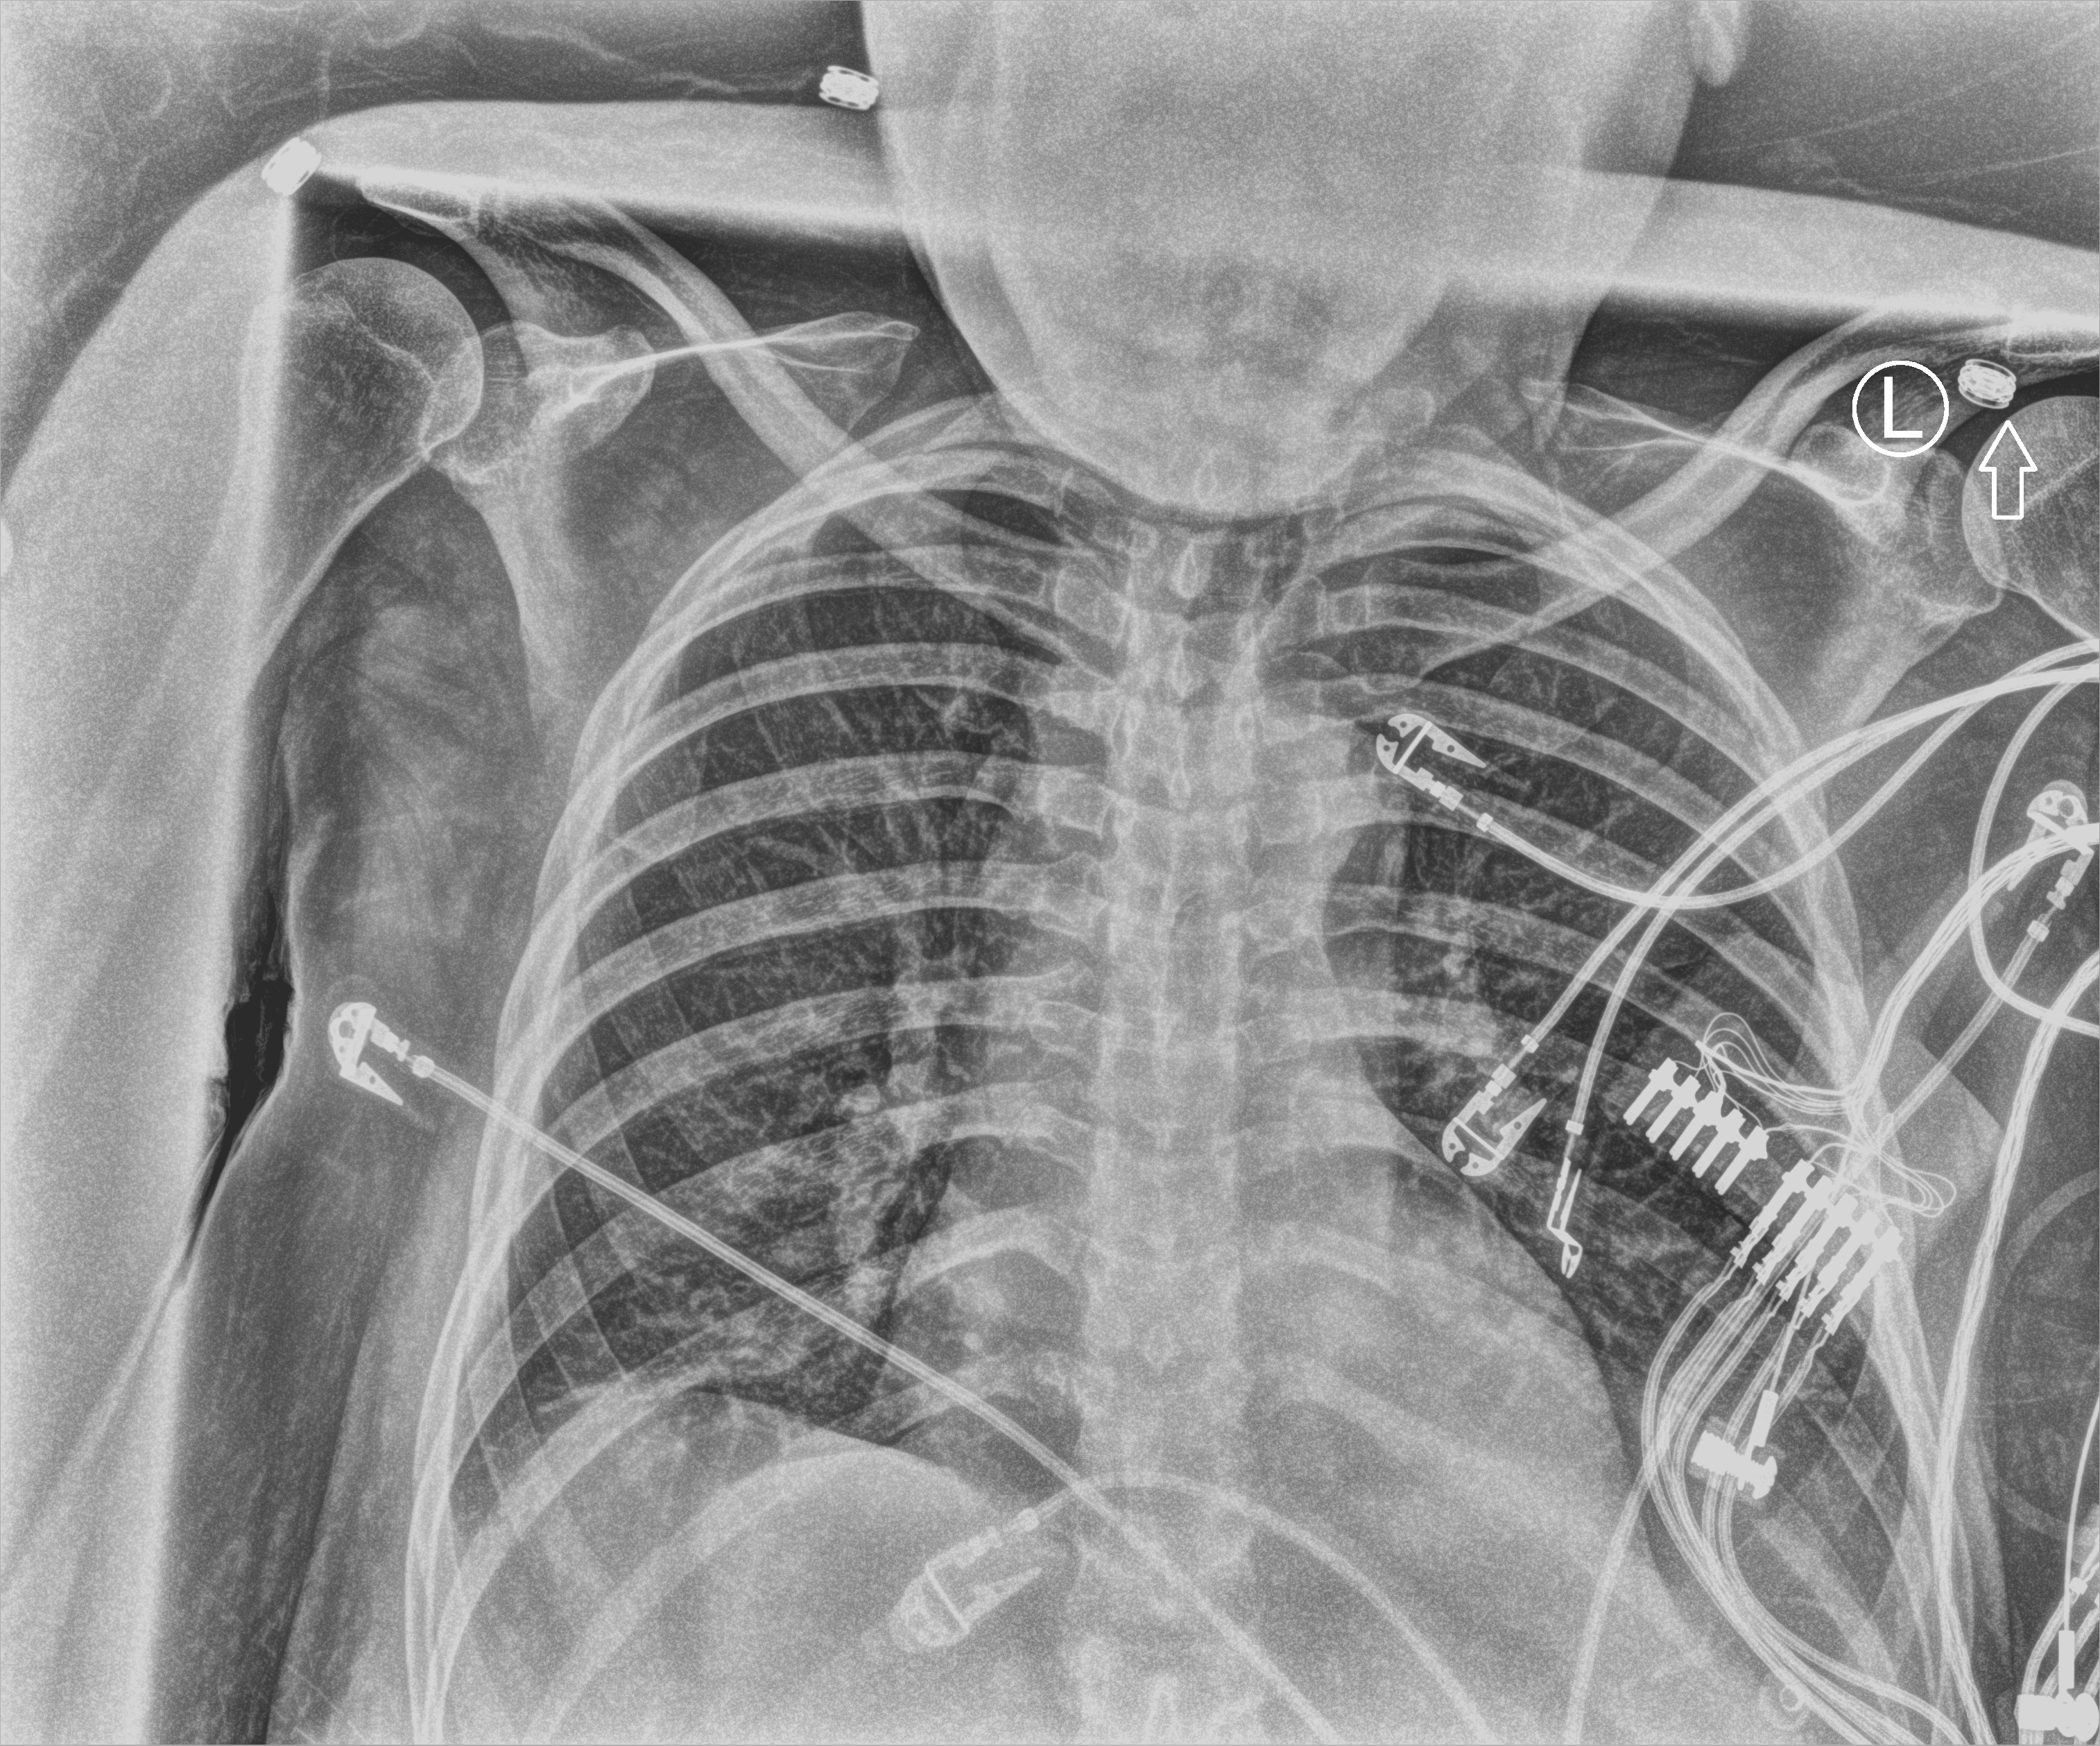
Portable chest radiograph; anteroposterior (AP) projection. Female patient hospitalised with COVID-19, age 18–59 years.
From the hospital-stay record, not from the radiograph (when in the stay this image was taken is not recorded): admitted to intensive care during this hospital stay: no; hypertension (admission record): yes.